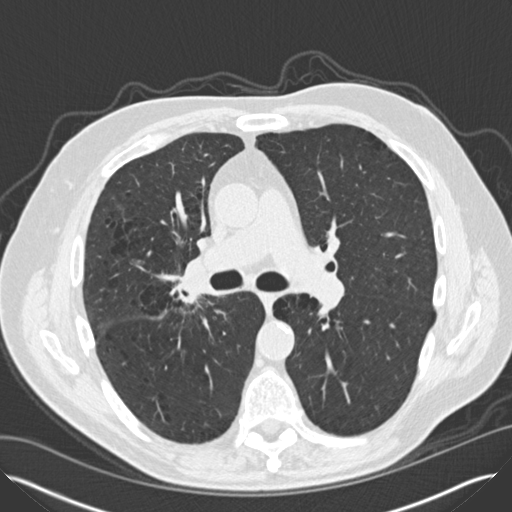
Low-dose screening chest CT, axial slice; second screening round (one year after baseline); lung window (W 1500 / L -600 HU); 2 mm slice thickness; standard (soft-tissue) reconstruction kernel (B30f); 120 kVp; 512 × 512 image matrix. Male, age 65 years at enrolment.
• Expert-annotated lung lesion, bounding box [x1, y1, x2, y2] px = [161, 262, 217, 316].
• Screening reader's record for this exam (one nodule recorded; not confirmed to be the boxed lesion): non-calcified nodule or mass ≥4 mm, left lower lobe, 12 × 8 mm, smooth margins, soft tissue attenuation, pre-existing on the prior screen: yes; interval growth: yes.
• Note: the box lies in the patient's right hemithorax on this image, whereas the reader's record names the left lung; they may be different findings.
• Official screen result: positive, other.
• Participant outcome: lung cancer diagnosed 67 days after this screen — non-small cell carcinoma, left lower lobe, right hilum, poorly differentiated (G3), stage IV (AJCC 6th edition), 5 mm at pathology.